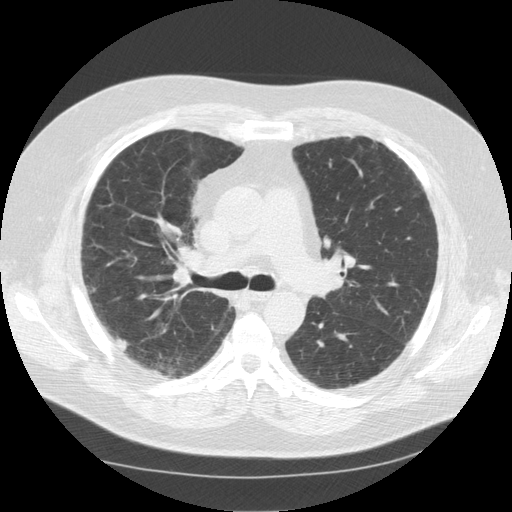
Axial slice from a low-dose chest CT screening exam; third annual screen; lung window (W 1500 / L -600 HU); 2.5 mm slice thickness; standard (soft-tissue) reconstruction kernel (STANDARD); slice 43 of 112 in the series. Male participant, aged 56 years at enrolment. Current smoker at enrolment.
Expert-annotated lung lesion, bounding box (x1, y1, x2, y2) in pixels: (104, 324, 139, 364). The screening reader recorded 2 non-calcified nodules or masses ≥4 mm on this exam (right upper lobe, right lower lobe); which of them this box marks is not recorded. Lung cancer was diagnosed 66 days after this screen: large cell neuroendocrine carcinoma, right upper lobe, stage IIIA (AJCC 6th edition), 10 mm at pathology.